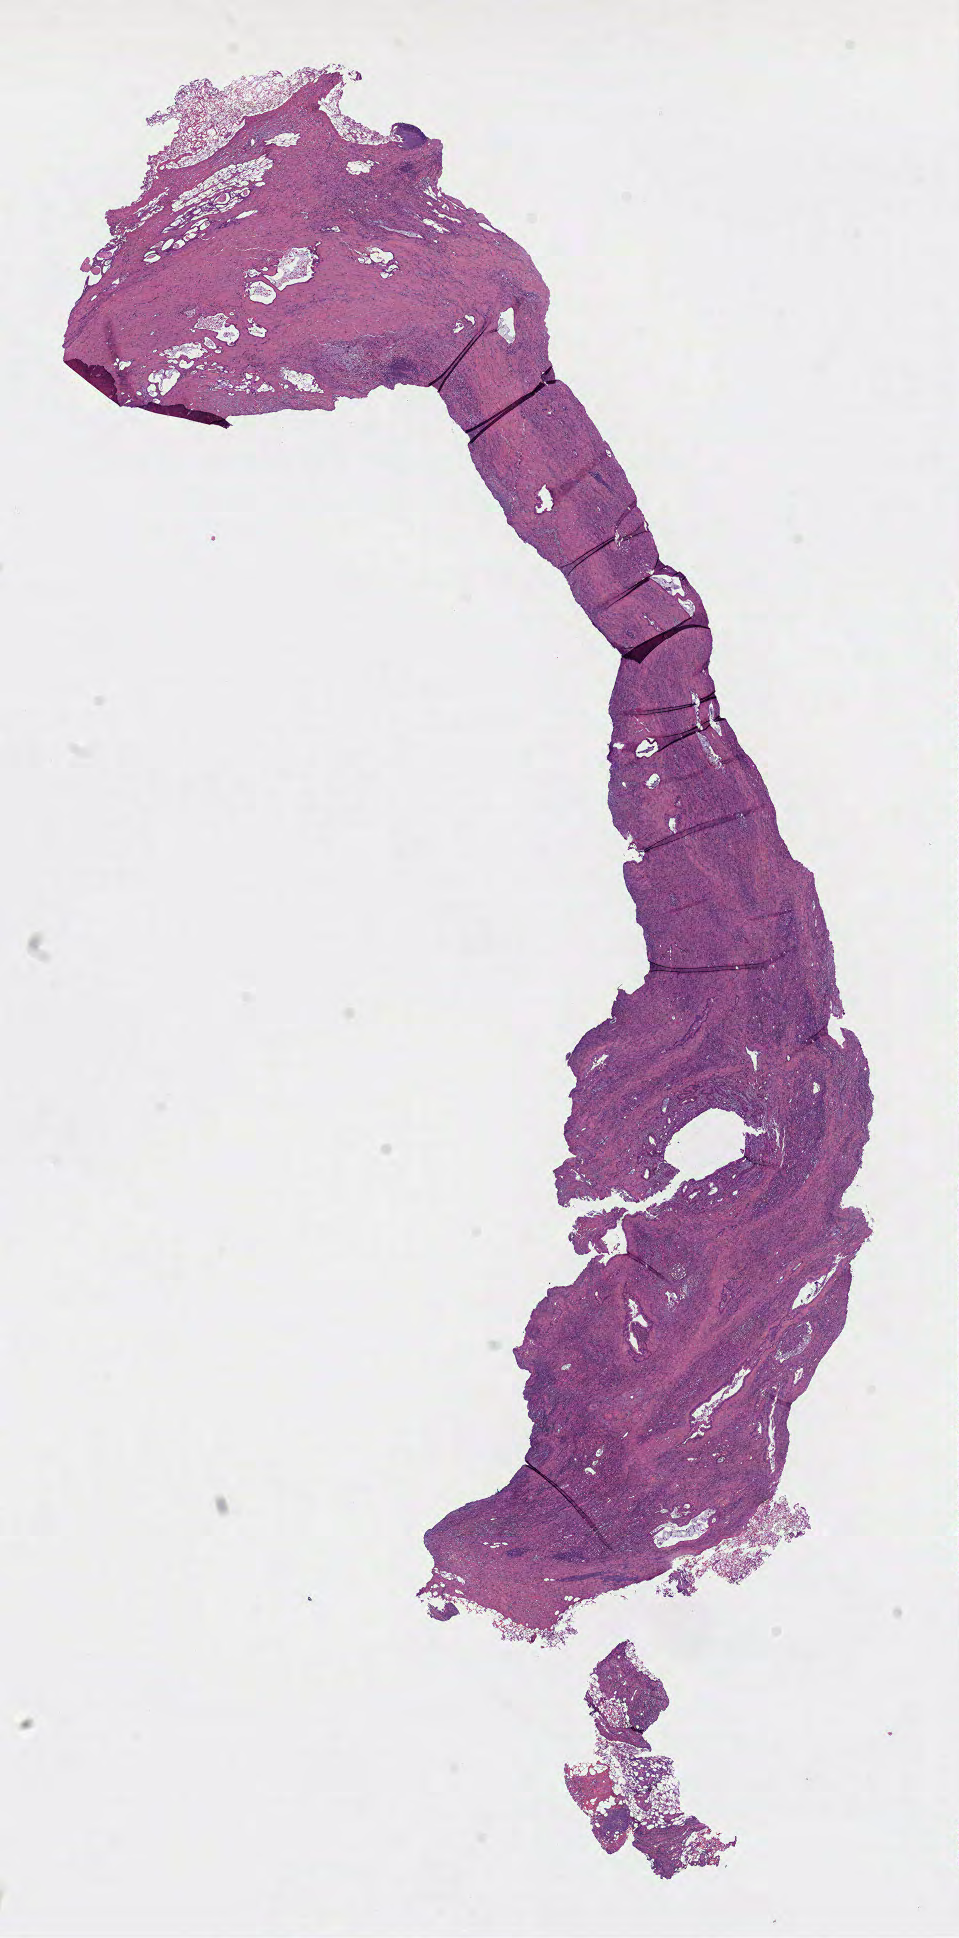
H&E whole-slide image, whole scanned area (about 7.7 x 15.6 mm) shown as a low-resolution overview, formalin-fixed paraffin-embedded (FFPE) diagnostic section, pancreas, primary tumour sample. Patient: male, age at initial diagnosis 70 years. Histologic grade: G2 (moderately differentiated).
Lymph nodes positive (case pathology): 0 of 1 examined. Histologic diagnosis: Adenocarcinoma, NOS (tail of pancreas). AJCC pathologic stage: IV (7th edition).